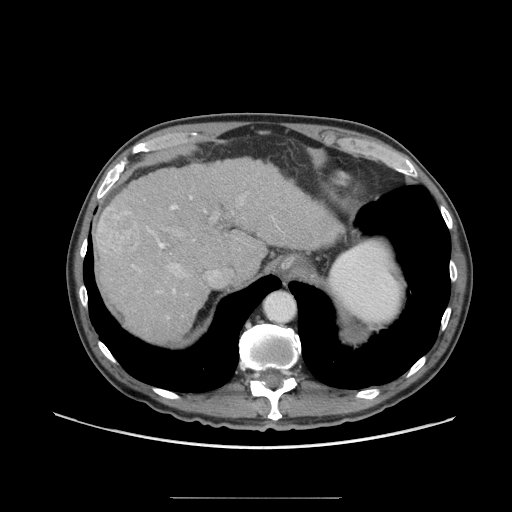
Contrast-enhanced abdominal CT (liver protocol), one axial slice. Position 52 of 71 along the scan axis. 140 kVp. Soft-tissue window (W 400 / L 40 HU). 2.5 mm slice thickness. 512 × 512 image matrix. From the clinical record (not read from this slice): diagnosis: hepatocellular carcinoma (patient treated with transarterial chemoembolisation; whether this scan precedes or follows treatment is not stated here); TNM stage (as recorded): Stage-I; Child-Pugh class: A; tumour differentiation: well differentiated; tumour nodularity: uninodular.
Structures marked on this image (semi-automatically segmented with operator editing):
- abdominal aorta: bounding box [x1, y1, x2, y2] px = [265, 292, 296, 322]
- liver parenchyma outside the tumour (the mass and vessels are separate outlines, so this box may not span the whole liver): [94, 158, 340, 342]
- mass: [95, 206, 152, 263]
- liver vessels: [131, 196, 219, 295]